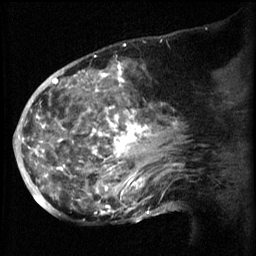
Breast MRI (dynamic contrast-enhanced), one sagittal slice; slice 31 of 60 in the series (ordered by position); 3 images stored at this slice position (order not interpretable as contrast timing); 1.5 T; TE 4.2 ms, TR 8.2 ms; 2.3 mm slice thickness; 256 × 256 image matrix, field of view 200 × 200 mm. Patient: female, 50 years.
Annotated regions visible in this slice (semi-automatic segmentation, software-assisted and operator-edited):
- analysis volume of interest (the breast-tissue region the enhancement analysis was run in; not a lesion): bounding box [x1, y1, x2, y2] px = [50, 64, 169, 217]
- tumour enhancement mask (voxels above the 70 % enhancement threshold inside the analysis volume of interest): [50, 64, 165, 215]